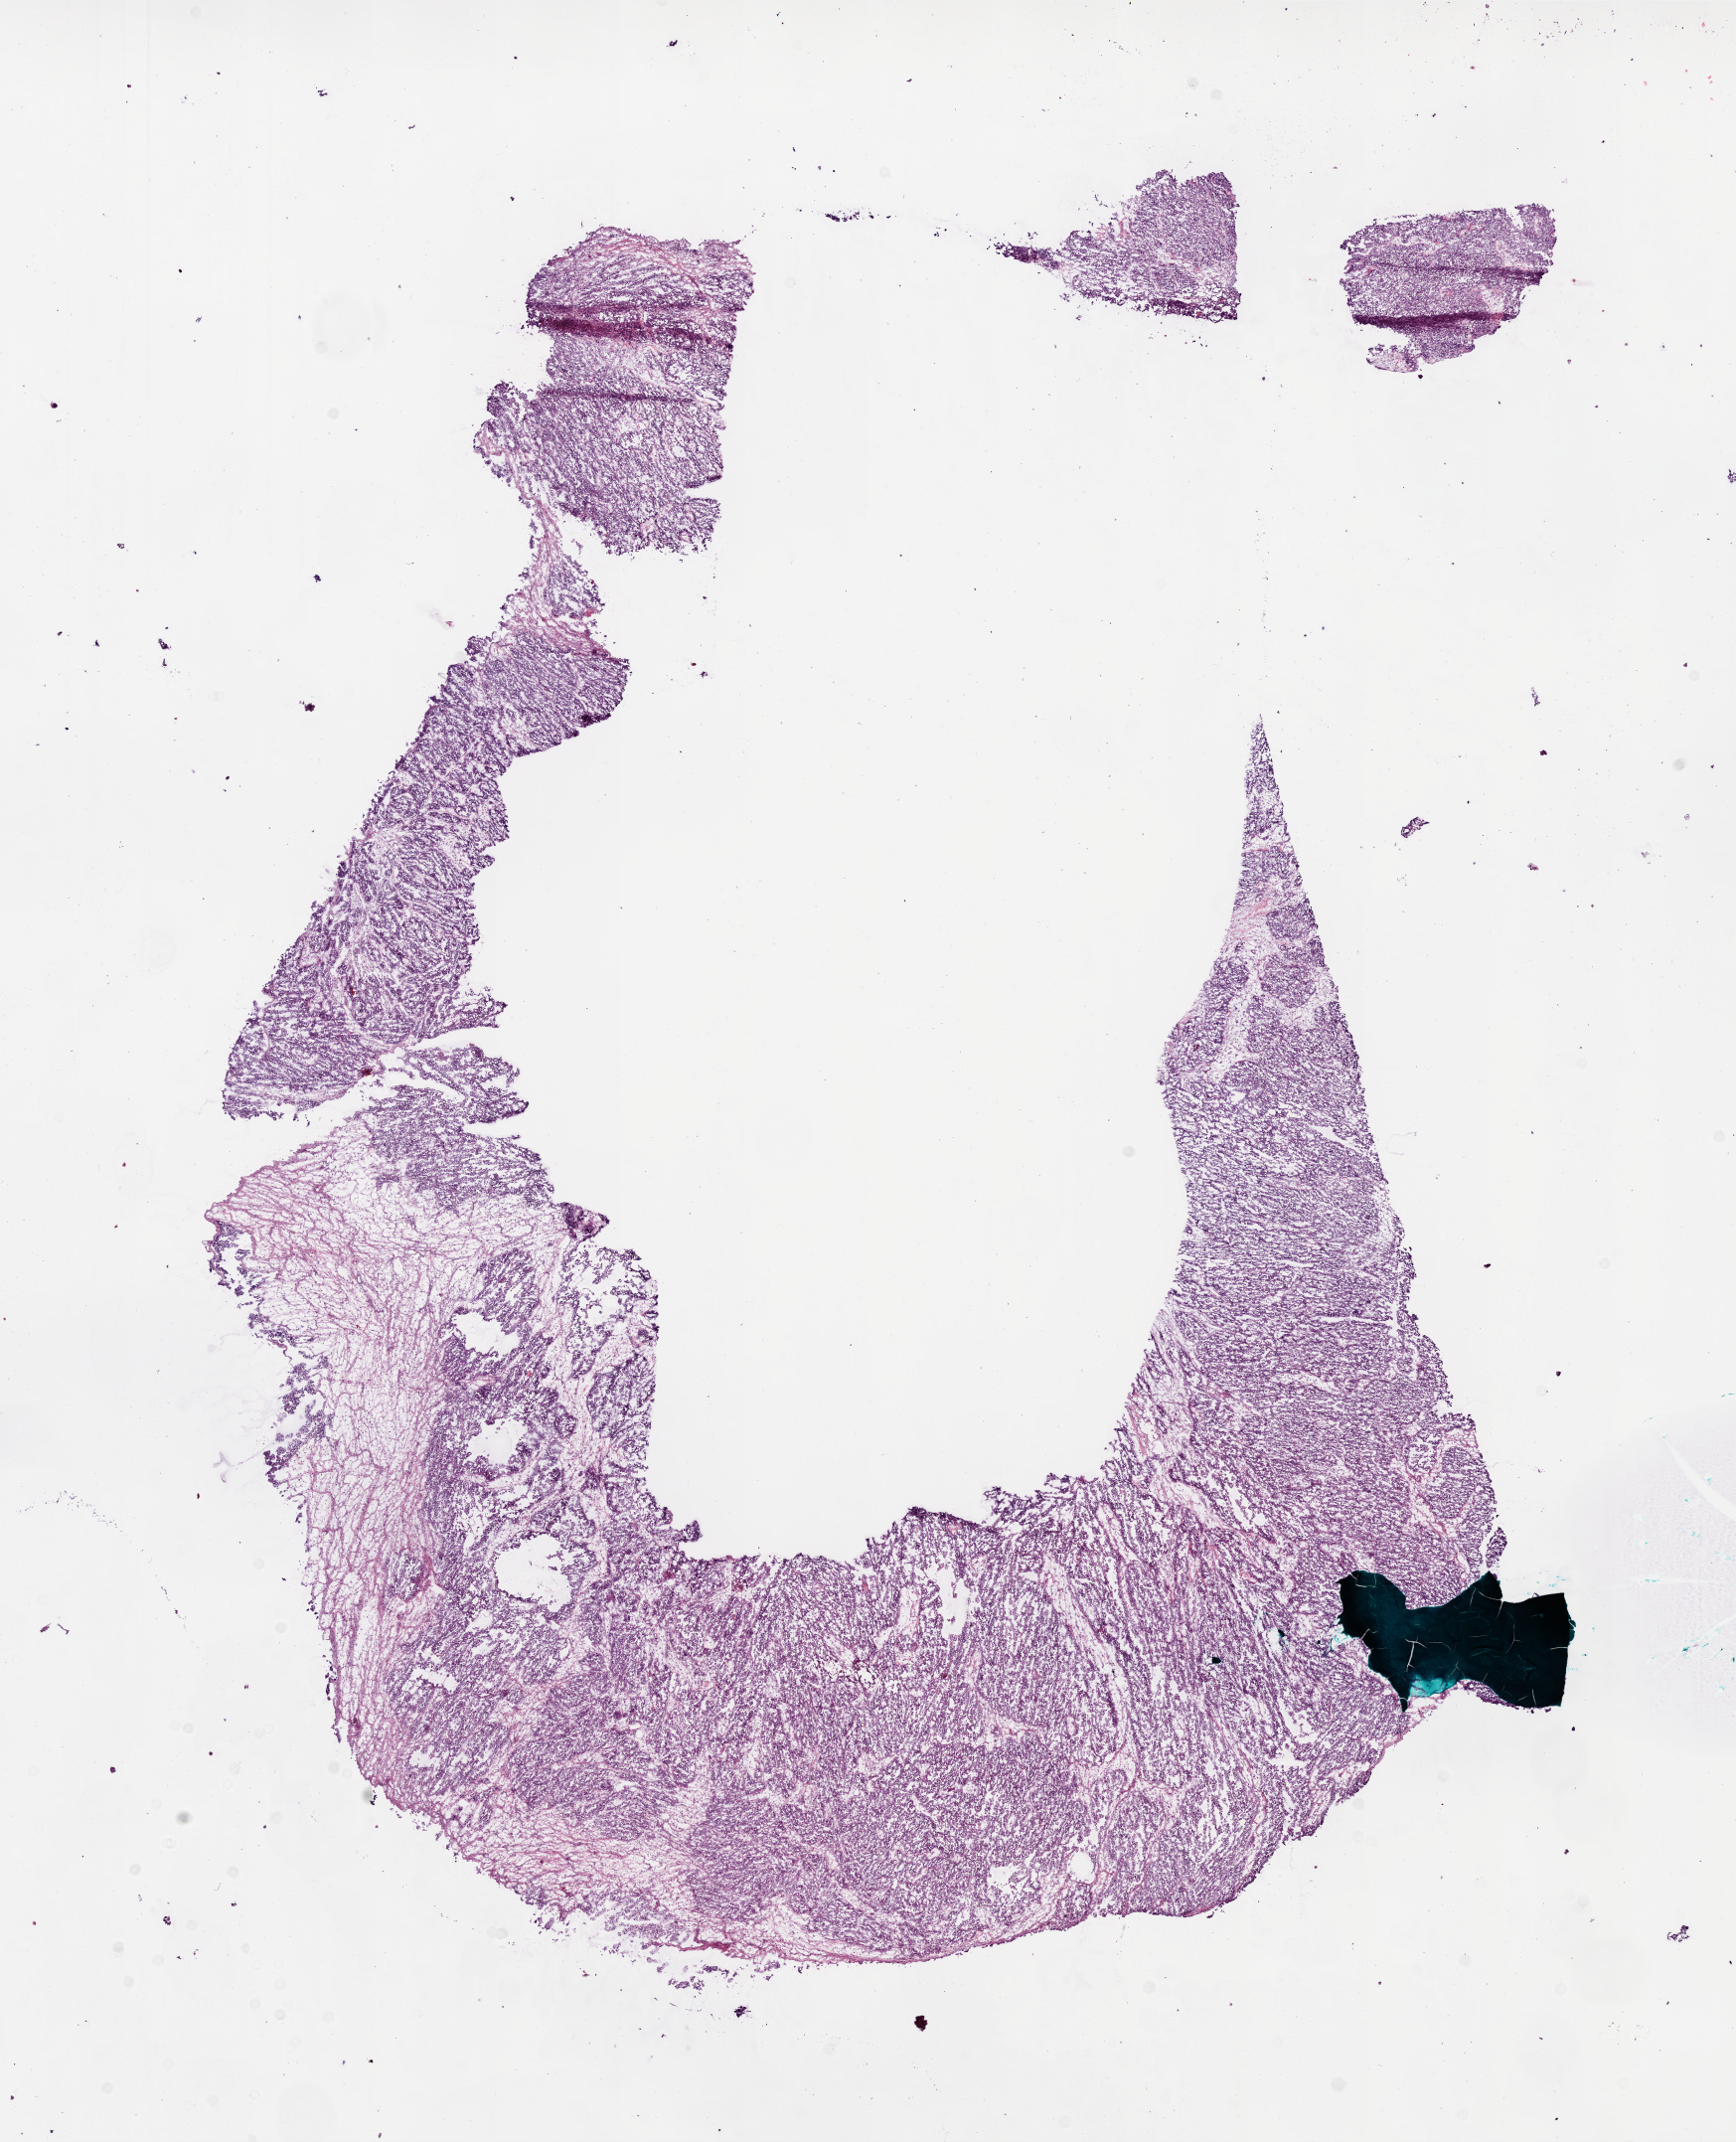
H&E-stained whole-slide image — low-resolution overview of the scanned area, about 14.0 x 17.3 mm, frozen section, sample: primary tumour, ovary. Female patient; age at initial diagnosis 61 years. Histologic grade: G3 (poorly differentiated). Slide review estimates, as recorded: tumour cells 78%, tumour nuclei 80%, normal cells 20%, stromal cells 0%, necrosis 2%.
* laterality: bilateral
* diagnosis: Serous cystadenocarcinoma, NOS
* FIGO stage: IIIC